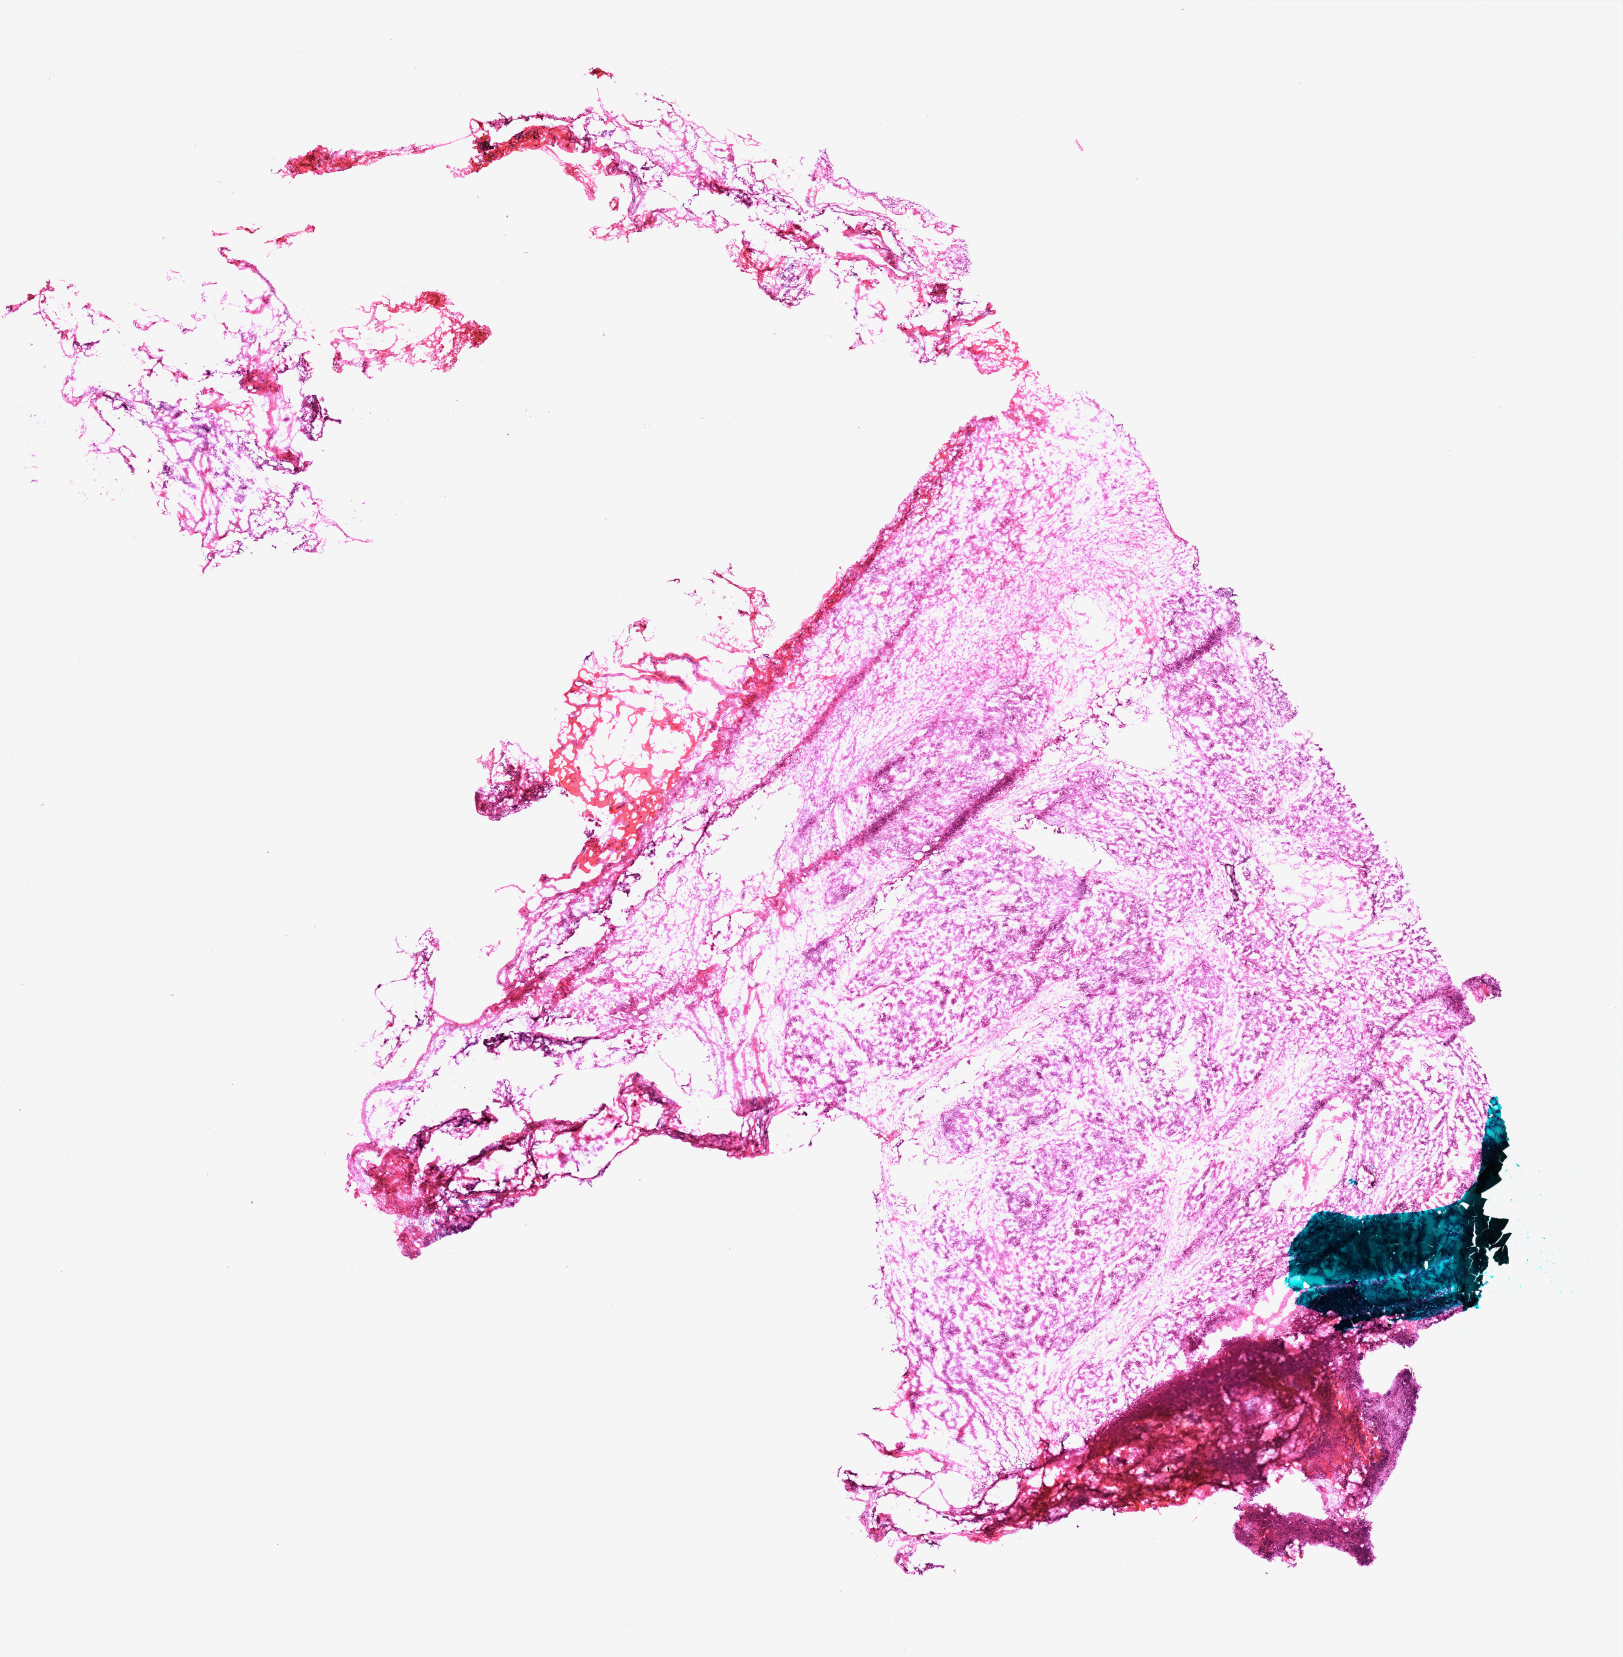
Whole-slide histology image, H&E-stained — a low-resolution overview of the entire scanned area, about 13.0 x 13.3 mm; frozen section; ovary, primary tumour sample. Female patient; age at initial diagnosis 58 years. Histologic grade: G3 (poorly differentiated). Pathologist review of this section (percent, as recorded): tumour nuclei 80%, normal cells 0%, stromal cells 0%, necrosis 10%.
• FIGO stage: IIIC
• histologic diagnosis: Serous cystadenocarcinoma, NOS